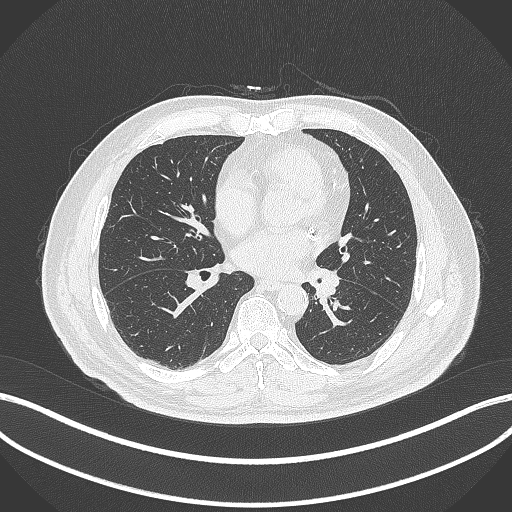
Chest CT, one axial slice; position 129 of 312 along the scan axis; lung window (W 1500 / L -600 HU); 512 × 512 image matrix, field of view 400 × 400 mm. Patient: male, 71 years. Case-level facts recorded for this patient, not image findings: clinical TNM (as recorded): T1b N0 M0.
Structures marked on this image (rectangle marked by the reading radiologist):
- lung tumour (recorded histology: squamous cell carcinoma): bounding box (x1, y1, x2, y2) in pixels: (316, 269, 341, 302)